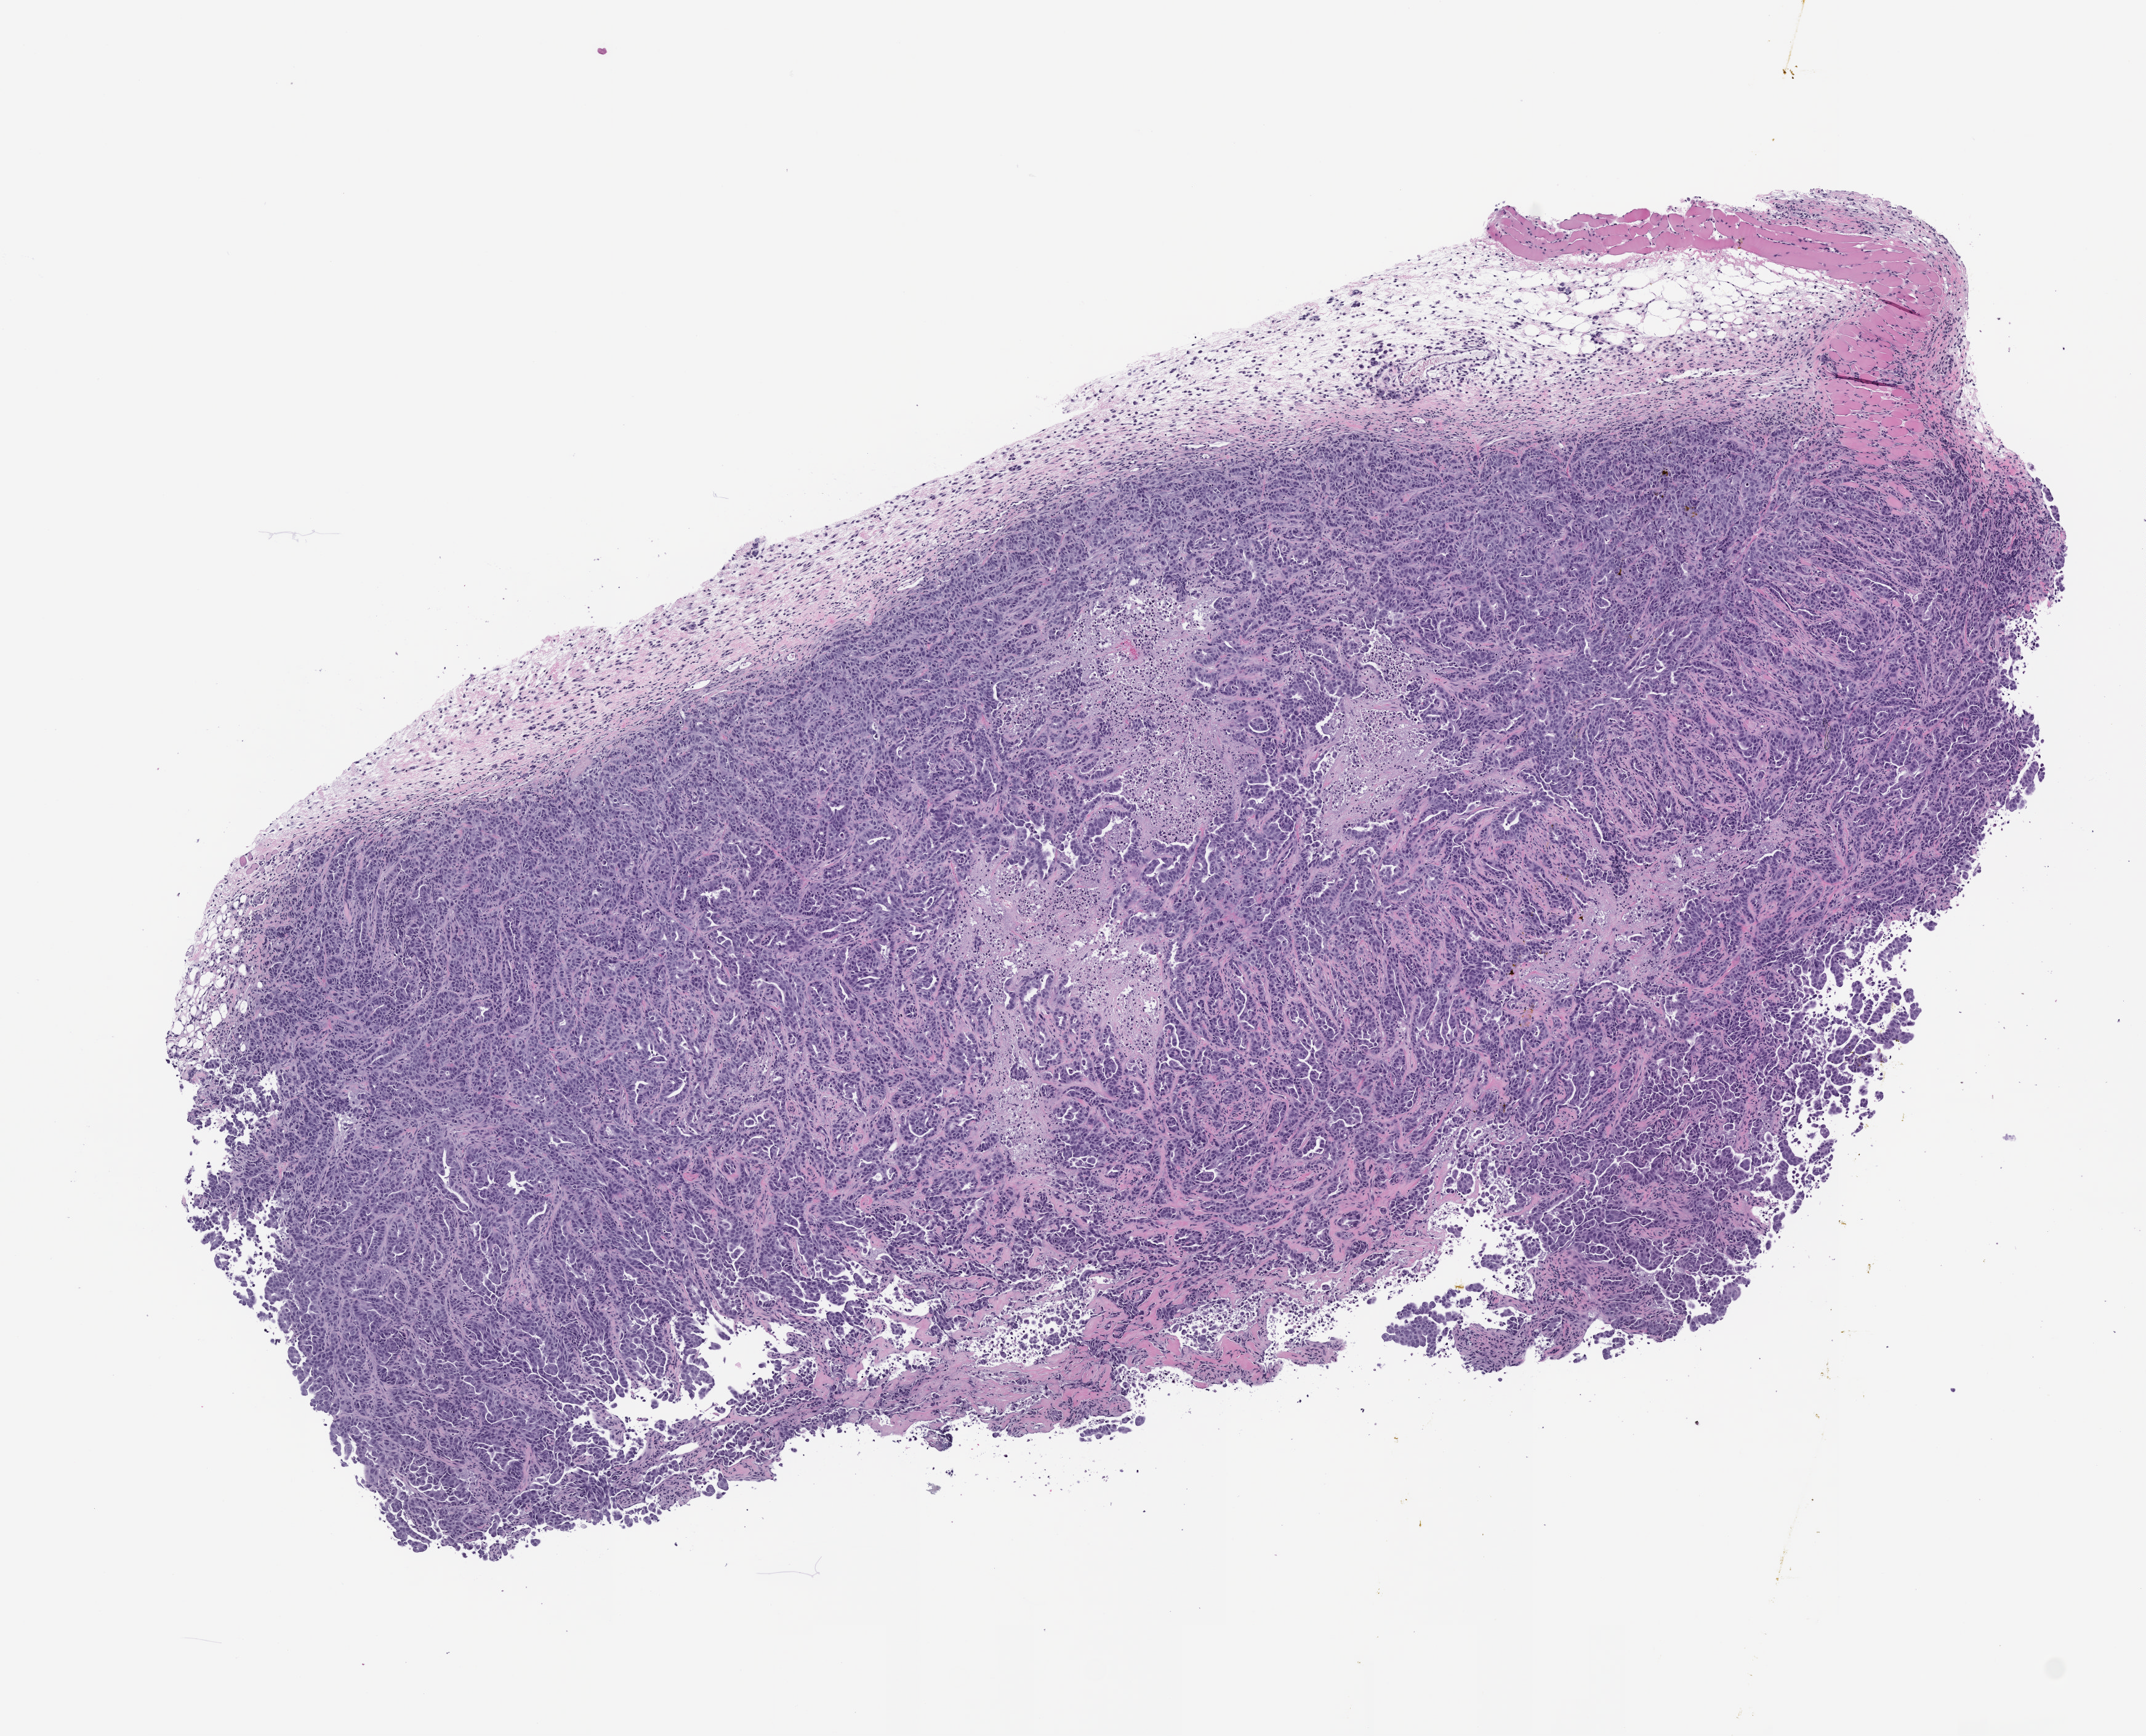
Hematoxylin and eosin (H&E) whole-slide image of a patient-derived xenograft (PDX) tumor grown in a mouse, a low-resolution overview of the entire scanned area, about 7.0 x 5.7 mm, FFPE section, originating tumor site category: lung.
Originating patient diagnosis: Lung Adenocarcinoma.